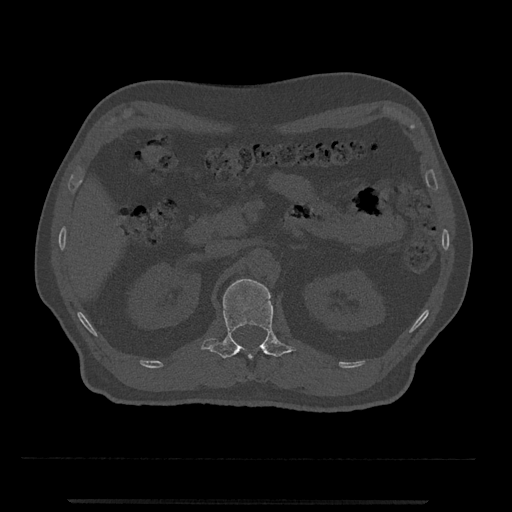
CT including the spine, one axial slice. Slice 343 of 797 in the series (ordered by position). Reconstruction kernel Br40s/3. Bone window (W 1800 / L 400 HU). 0.5 mm slice thickness. 512 × 512 image matrix, field of view 419 × 419 mm. Male patient, age 63 years. Case-level facts recorded for this patient, not image findings: primary cancer: prostate.
Outlined on this slice (semi-automatically segmented with operator editing):
- L1 vertebra: bounding box (x1, y1, x2, y2) in pixels: (201, 278, 296, 359)